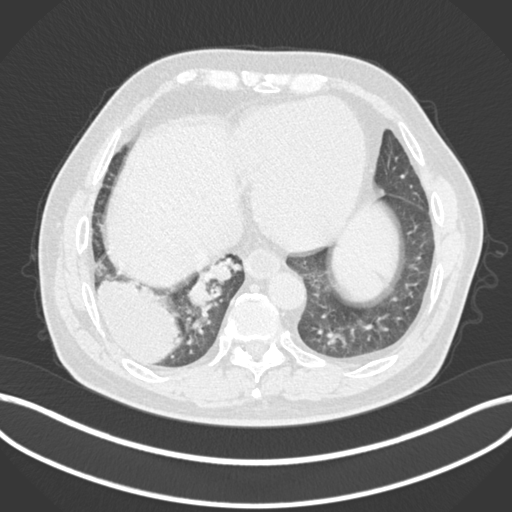
Chest CT, one axial slice; position 33 of 200 along the scan axis; reconstruction kernel B30f; 120 kVp; lung window (W 1500 / L -600 HU); 512 × 512 image matrix. Patient: male, 59 years.
Outlined on this slice (rectangle marked by the reading radiologist):
- lung tumour (recorded histology: adenocarcinoma): box from (x=92, y=277) to (x=185, y=367) px